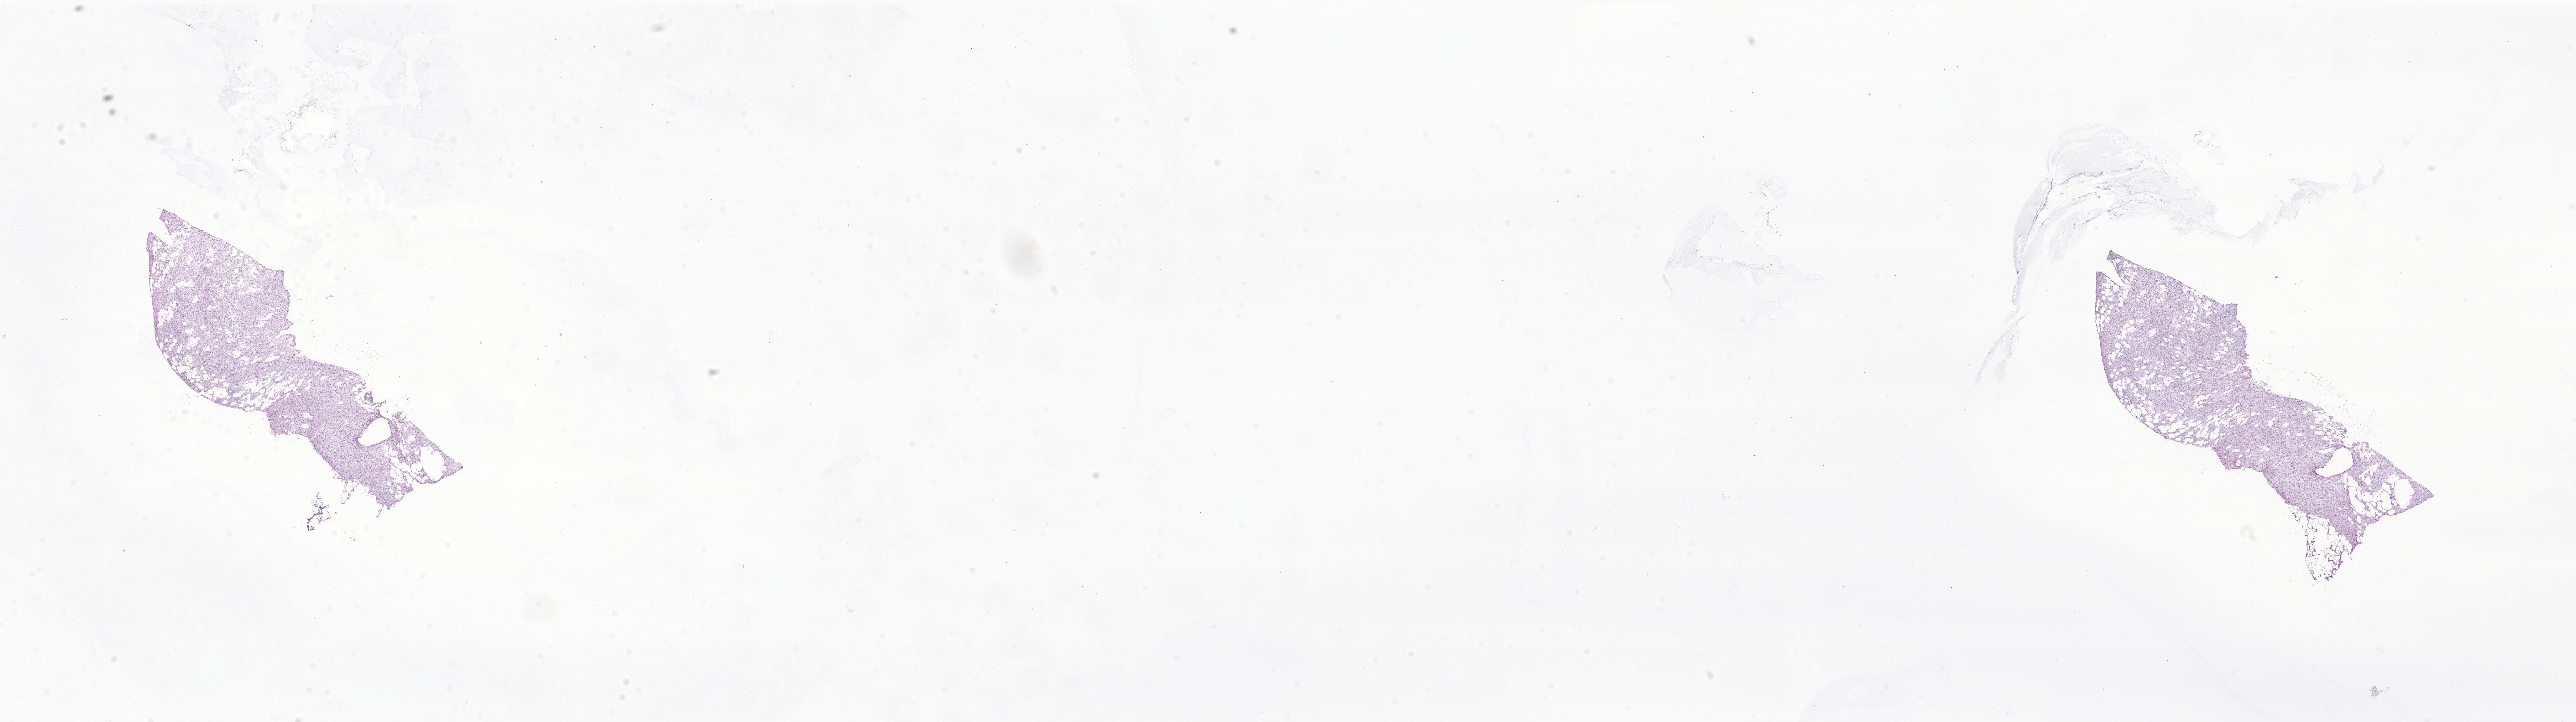
Haematoxylin and eosin whole-slide image of tumor tissue from the soft tissue of trunk, low-resolution overview of the scanned area, about 34.7 x 9.7 mm; frozen section. Patient: male, age 191 months.
Diagnosis (ICD-O-3 morphology term): Dermatofibrosarcoma protuberans, fibrosarcomatous. Tissue or organ of origin (case record): connective, subcutaneous and other soft tissues of trunk.